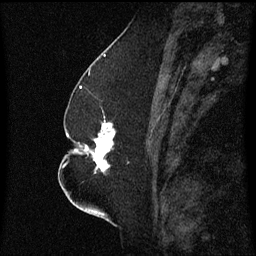
Breast MRI (dynamic contrast-enhanced), one sagittal slice. Position 28 of 60 along the scan axis. Dynamic contrast-enhanced series, image 2 of 3 at this slice position (ordered by acquisition). 1.5 T. TE 4.2 ms, TR 8.4 ms. 2.3 mm slice thickness. 256 × 256 image matrix. Female patient, age 52 years. From the clinical record (not read from this slice): setting: breast cancer imaged before/during neoadjuvant chemotherapy; receptor status: HR-positive, HER2-negative.
Structures marked on this image (semi-automatically segmented with operator editing):
- analysis volume of interest (the breast-tissue region the enhancement analysis was run in; not a lesion): box from (x=75, y=122) to (x=129, y=175) px
- tumour enhancement mask (voxels above the 70 % enhancement threshold inside the analysis volume of interest): (x=79, y=124)–(x=115, y=173)